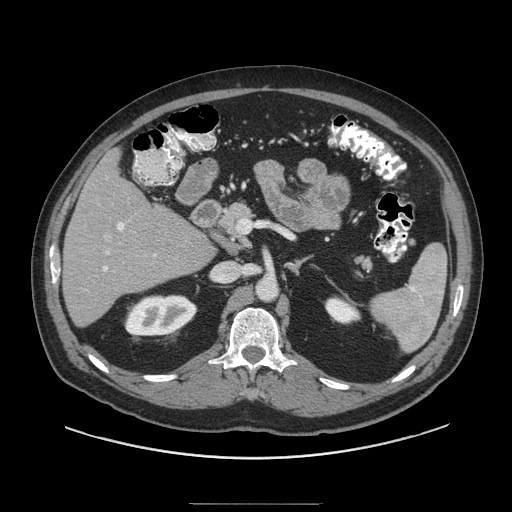
Contrast-enhanced abdominal CT (liver protocol), one axial slice; position 48 of 91 along the scan axis; soft-tissue window (W 400 / L 40 HU); 2.5 mm slice thickness; 512 × 512 image matrix. From the clinical record (not read from this slice): diagnosis: hepatocellular carcinoma (patient treated with transarterial chemoembolisation; whether this scan precedes or follows treatment is not stated here); TNM stage (as recorded): Stage-I; Child-Pugh class: A; tumour differentiation: well differentiated; tumour size: 4 cm.
Structures marked on this image (semi-automatically segmented with operator editing):
- liver parenchyma outside the tumour (the mass and vessels are separate outlines, so this box may not span the whole liver): bounding box (x1, y1, x2, y2) in pixels: (62, 148, 214, 326)
- liver vessels: (103, 222, 157, 272)